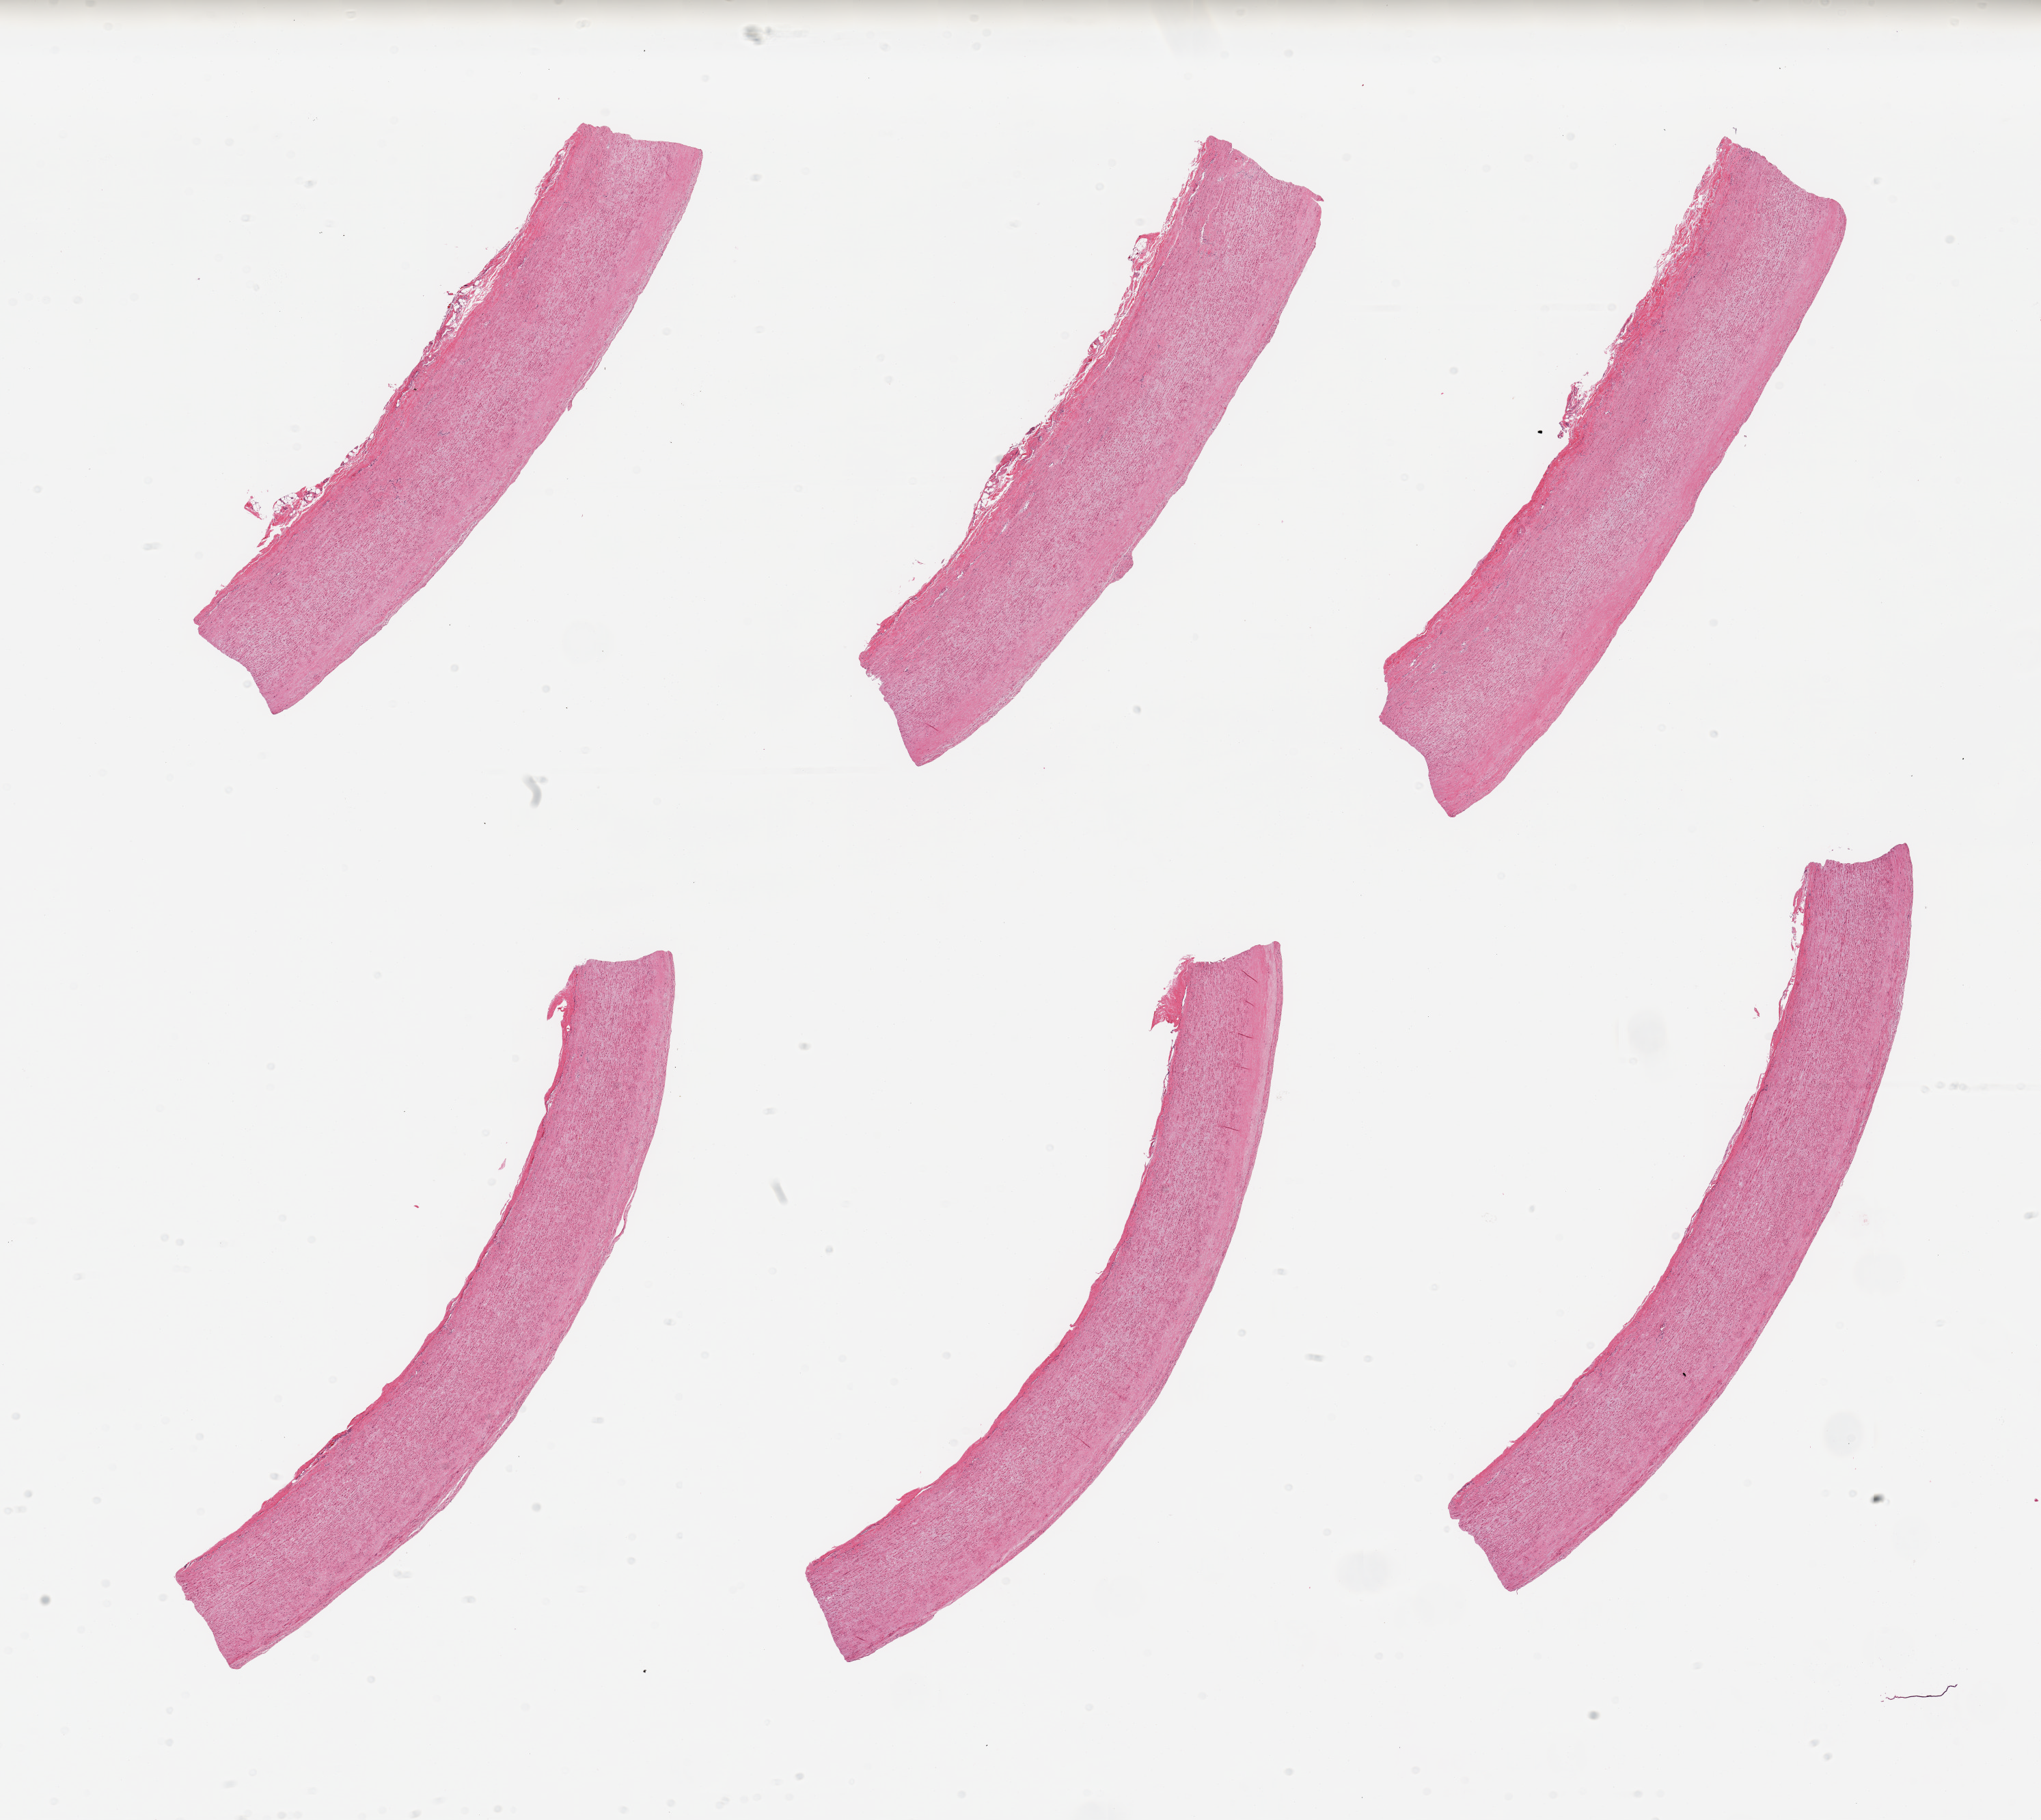
Haematoxylin and eosin whole-slide image, low-resolution overview of the scanned area, about 23.6 x 21.1 mm, PAXgene-fixed paraffin-embedded (PFPE) section, sampled site (target tissue): aorta, donor tissue sample. Donor sex: male.
Review note (as recorded): 6 pieces, no significant atherosis.